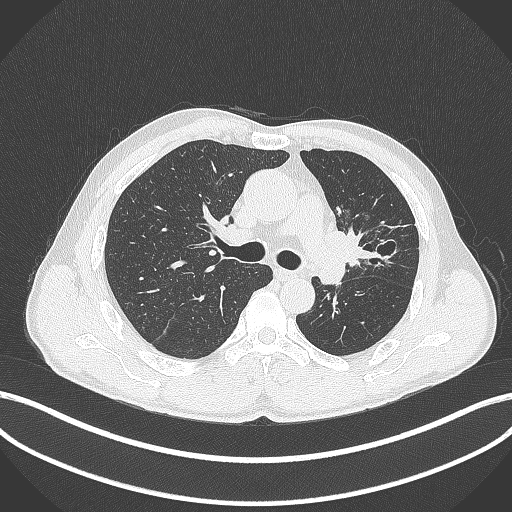
Chest CT, one axial slice. Slice 266 of 429 in the series (ordered by position). Reconstruction kernel B70f. 120 kVp. Lung window (W 1500 / L -600 HU). 1 mm slice thickness. 512 × 512 image matrix, field of view 400 × 400 mm. Patient: male, 57 years. Case-level facts recorded for this patient, not image findings: clinical TNM (as recorded): T2b N0 M0.
Outlined on this slice (bounding box drawn by a radiologist):
- lung tumour (recorded histology: squamous cell carcinoma): bounding box <324,223,379,270> (left, top, right, bottom; pixels)